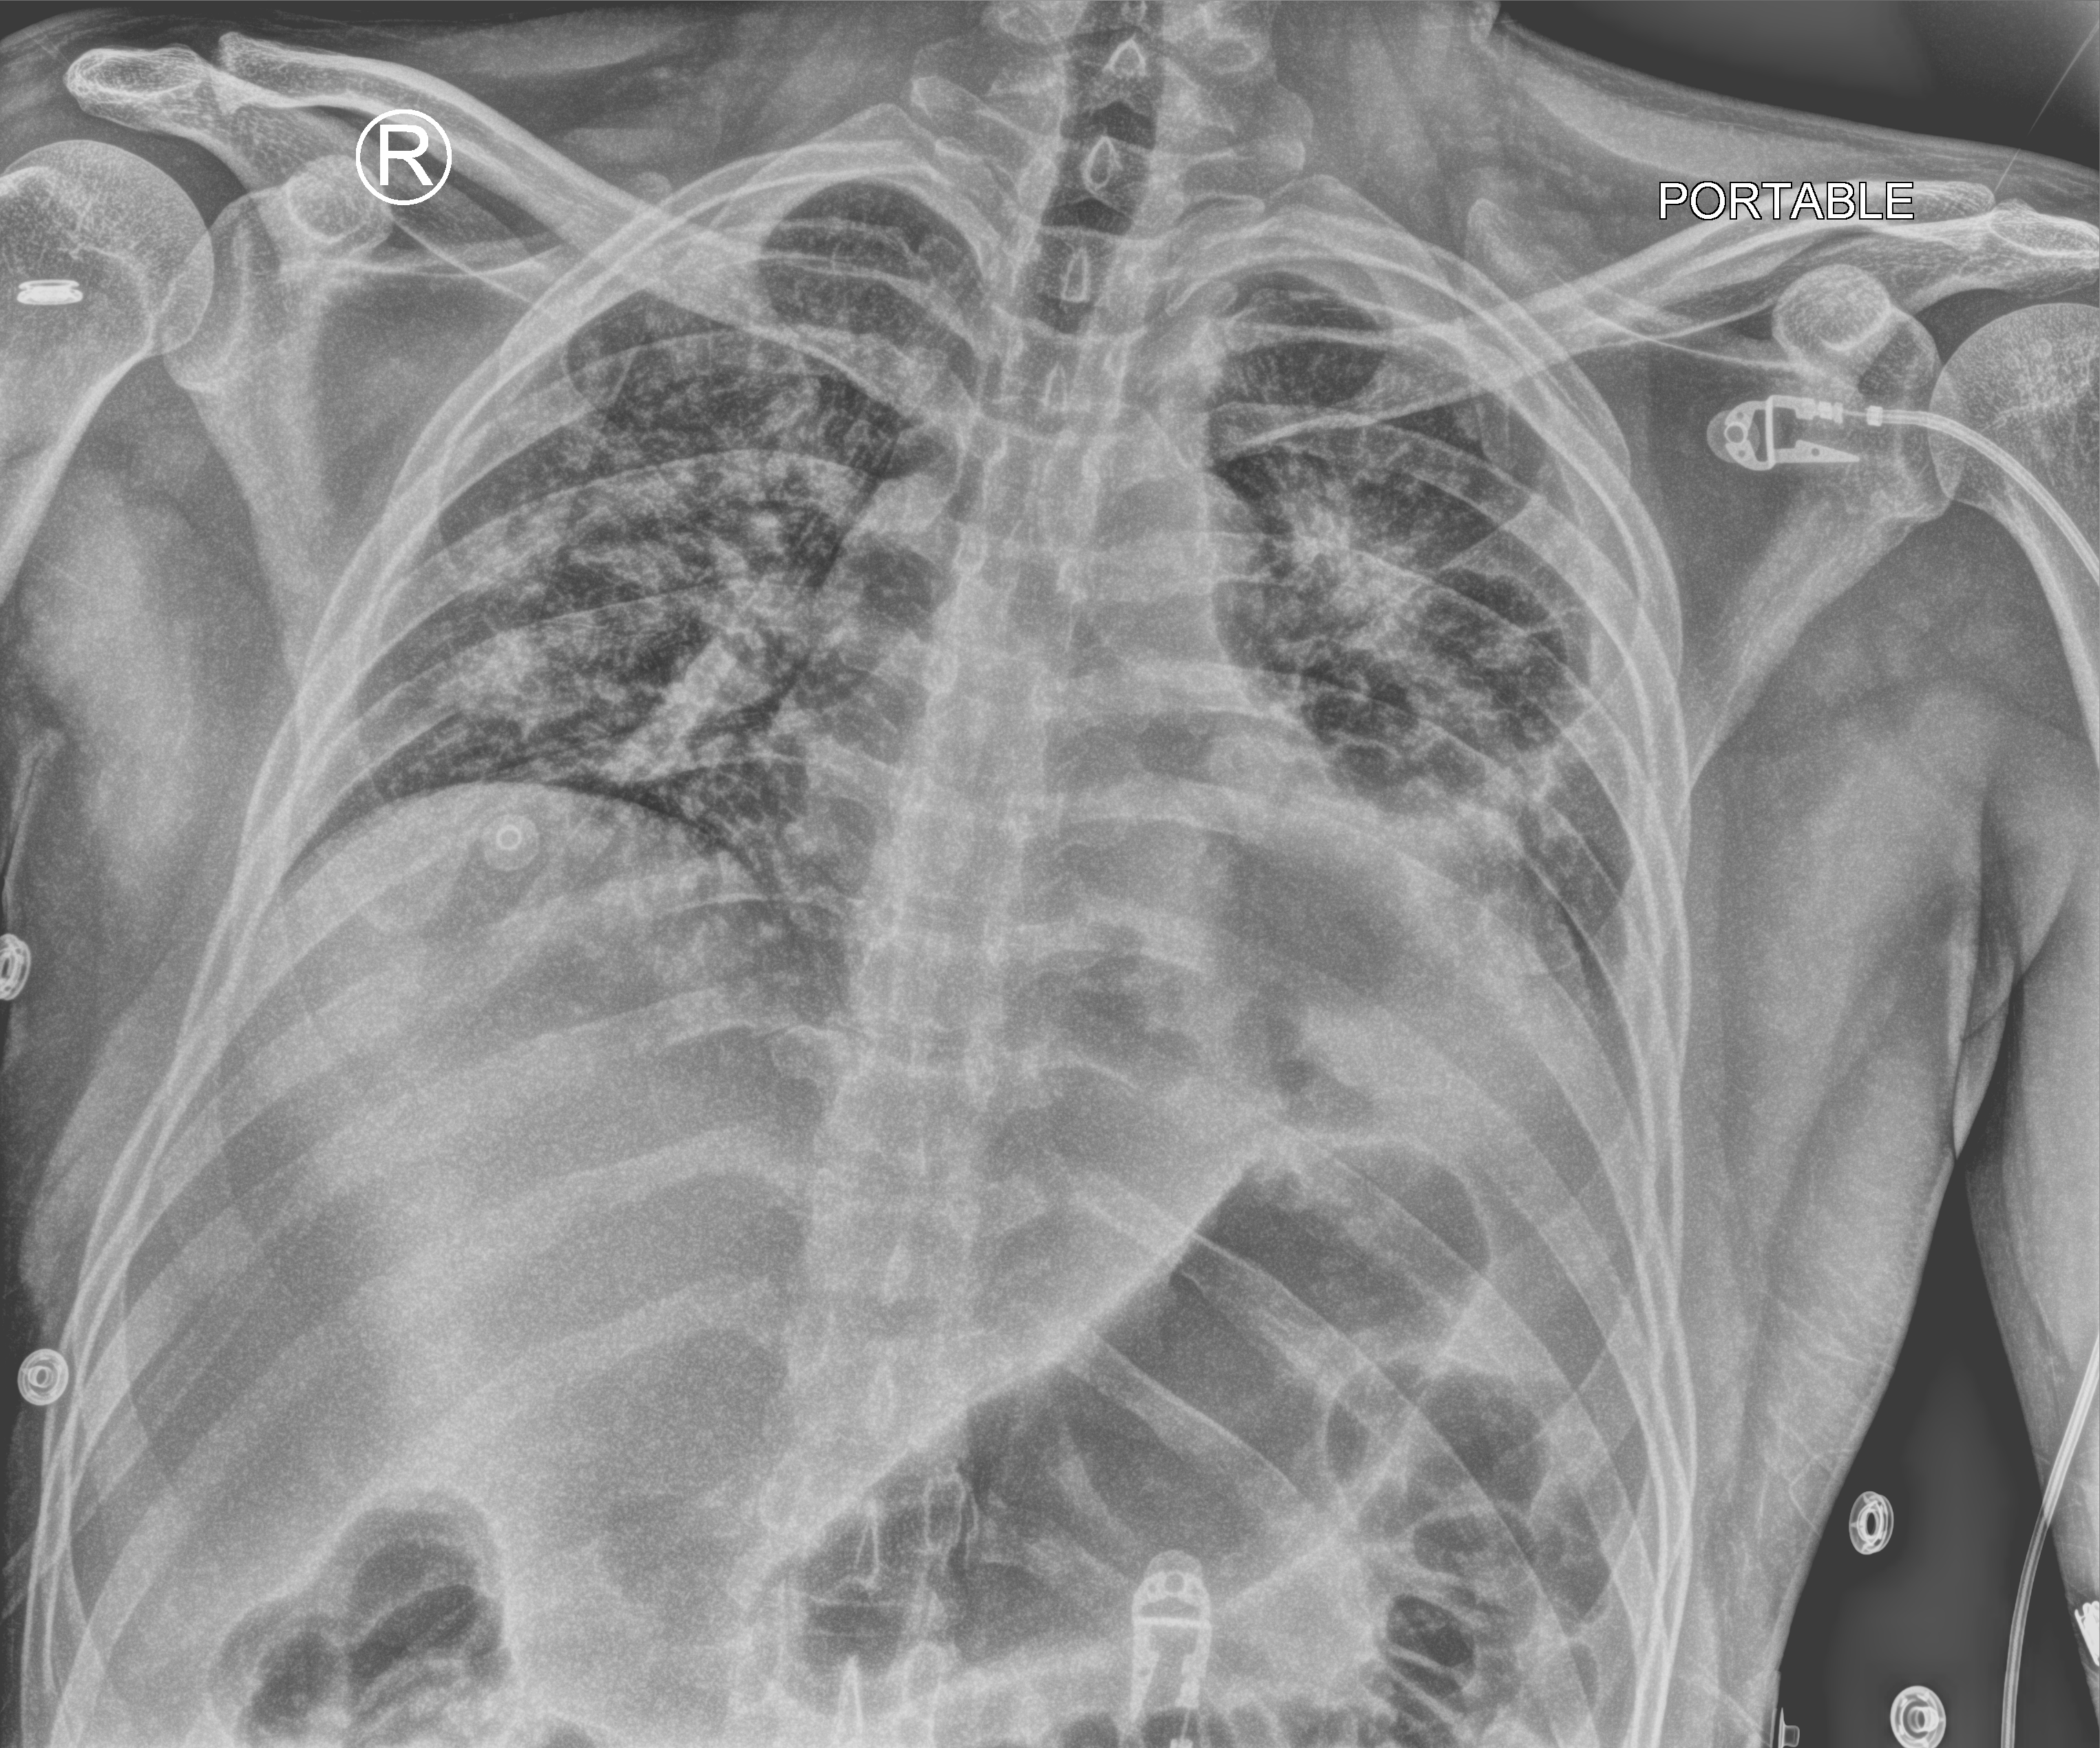
Bedside chest radiograph (computed radiography); anteroposterior (AP) projection. Male patient hospitalised with COVID-19, age 18–59 years.
From the hospital-stay record, not from the radiograph (when in the stay this image was taken is not recorded): mechanically ventilated during this hospital stay: yes; length of hospital stay: 31 days; smoking status (admission record): never.